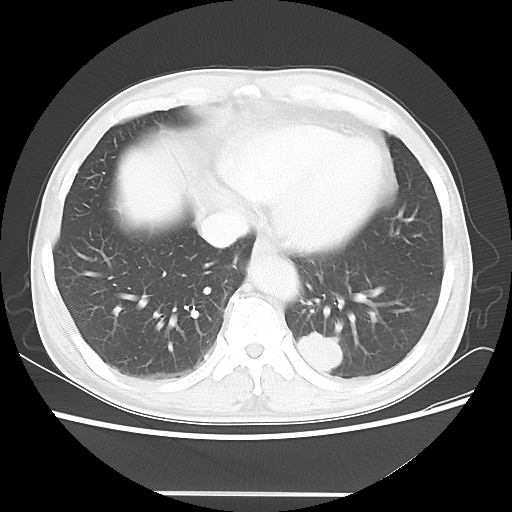
Chest CT, one axial slice; slice 16 of 60 in the series (ordered by position); reconstruction kernel LUNG; 100 kVp; lung window (W 1500 / L -600 HU); 512 × 512 image matrix. Male patient, age 55 years. Case-level facts recorded for this patient, not image findings: clinical TNM (as recorded): T1c N3 M0; histopathological grade: G3.
Outlined on this slice (bounding box drawn by a radiologist):
- lung tumour (recorded histology: small cell carcinoma): bounding box [x1, y1, x2, y2] px = [289, 321, 348, 377]